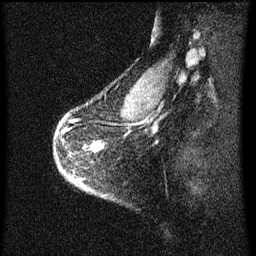
Breast MRI (dynamic contrast-enhanced), one sagittal slice. Slice 51 of 60 in the series (ordered by position). Dynamic contrast-enhanced series, image 2 of 3 at this slice position (ordered by acquisition). 1.5 T. TE 4.2 ms, TR 8 ms. 2 mm slice thickness. 256 × 256 image matrix, field of view 180 × 180 mm. Patient: female, 56 years.
Annotated regions visible in this slice (semi-automatic segmentation, software-assisted and operator-edited):
- analysis volume of interest (the breast-tissue region the enhancement analysis was run in; not a lesion): bounding box <58,116,101,189> (left, top, right, bottom; pixels)
- tumour enhancement mask (voxels above the 70 % enhancement threshold inside the analysis volume of interest): <98,144,101,147>